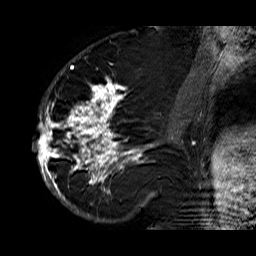
Breast MRI (dynamic contrast-enhanced), one sagittal slice. Position 28 of 60 along the scan axis. Dynamic contrast-enhanced series, time point 2 of 6 at this slice position (early post-contrast). 1.5 T. TE 6.3 ms, TR 32.9 ms. 4 mm slice thickness. 256 × 256 image matrix. Female patient. From the clinical record (not read from this slice): setting: breast cancer imaged before/during neoadjuvant chemotherapy; receptor status: HR-positive, HER2-negative.
Outlined on this slice (semi-automatically segmented with operator editing):
- analysis volume of interest (the breast-tissue region the enhancement analysis was run in; not a lesion): bounding box <33,74,176,210> (left, top, right, bottom; pixels)
- tumour enhancement mask (voxels above the 100 % enhancement threshold inside the analysis volume of interest): <33,81,176,210>